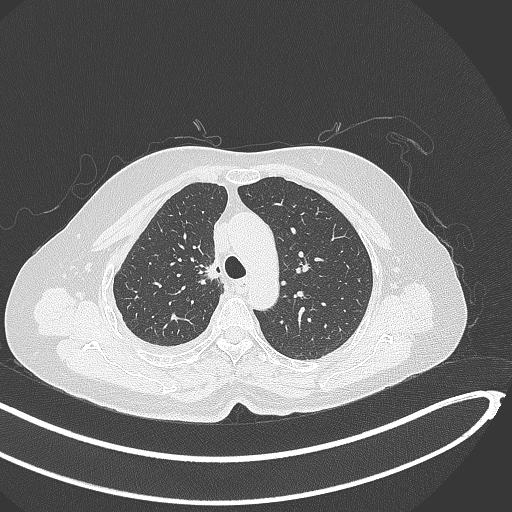
Chest CT, one axial slice; position 275 of 345 along the scan axis; reconstruction kernel B70f; 120 kVp; lung window (W 1500 / L -600 HU); 1 mm slice thickness; 512 × 512 image matrix, field of view 400 × 400 mm. Female patient, age 64 years. From the clinical record (not read from this slice): clinical TNM (as recorded): T1b N0 M1.
Annotated regions visible in this slice (rectangle marked by the reading radiologist):
- lung tumour (recorded histology: adenocarcinoma): bounding box [x1, y1, x2, y2] px = [200, 257, 223, 286]